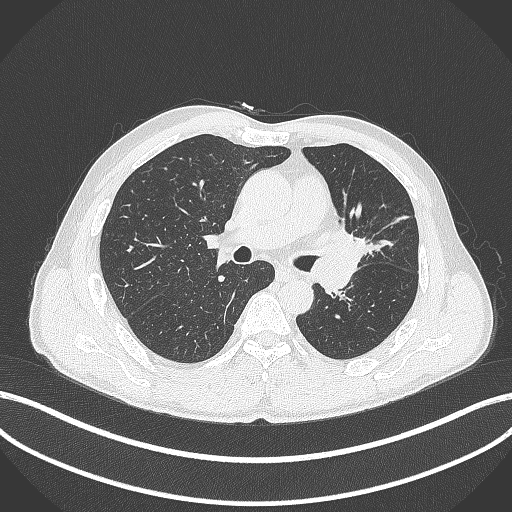
Chest CT, one axial slice. Position 249 of 429 along the scan axis. Reconstruction kernel B70f. Lung window (W 1500 / L -600 HU). 1 mm slice thickness. 512 × 512 image matrix, field of view 400 × 400 mm. Patient: male, 57 years. From the clinical record (not read from this slice): clinical TNM (as recorded): T2b N0 M0.
Structures marked on this image (rectangle marked by the reading radiologist):
- lung tumour (recorded histology: squamous cell carcinoma): box from (x=321, y=224) to (x=372, y=265) px